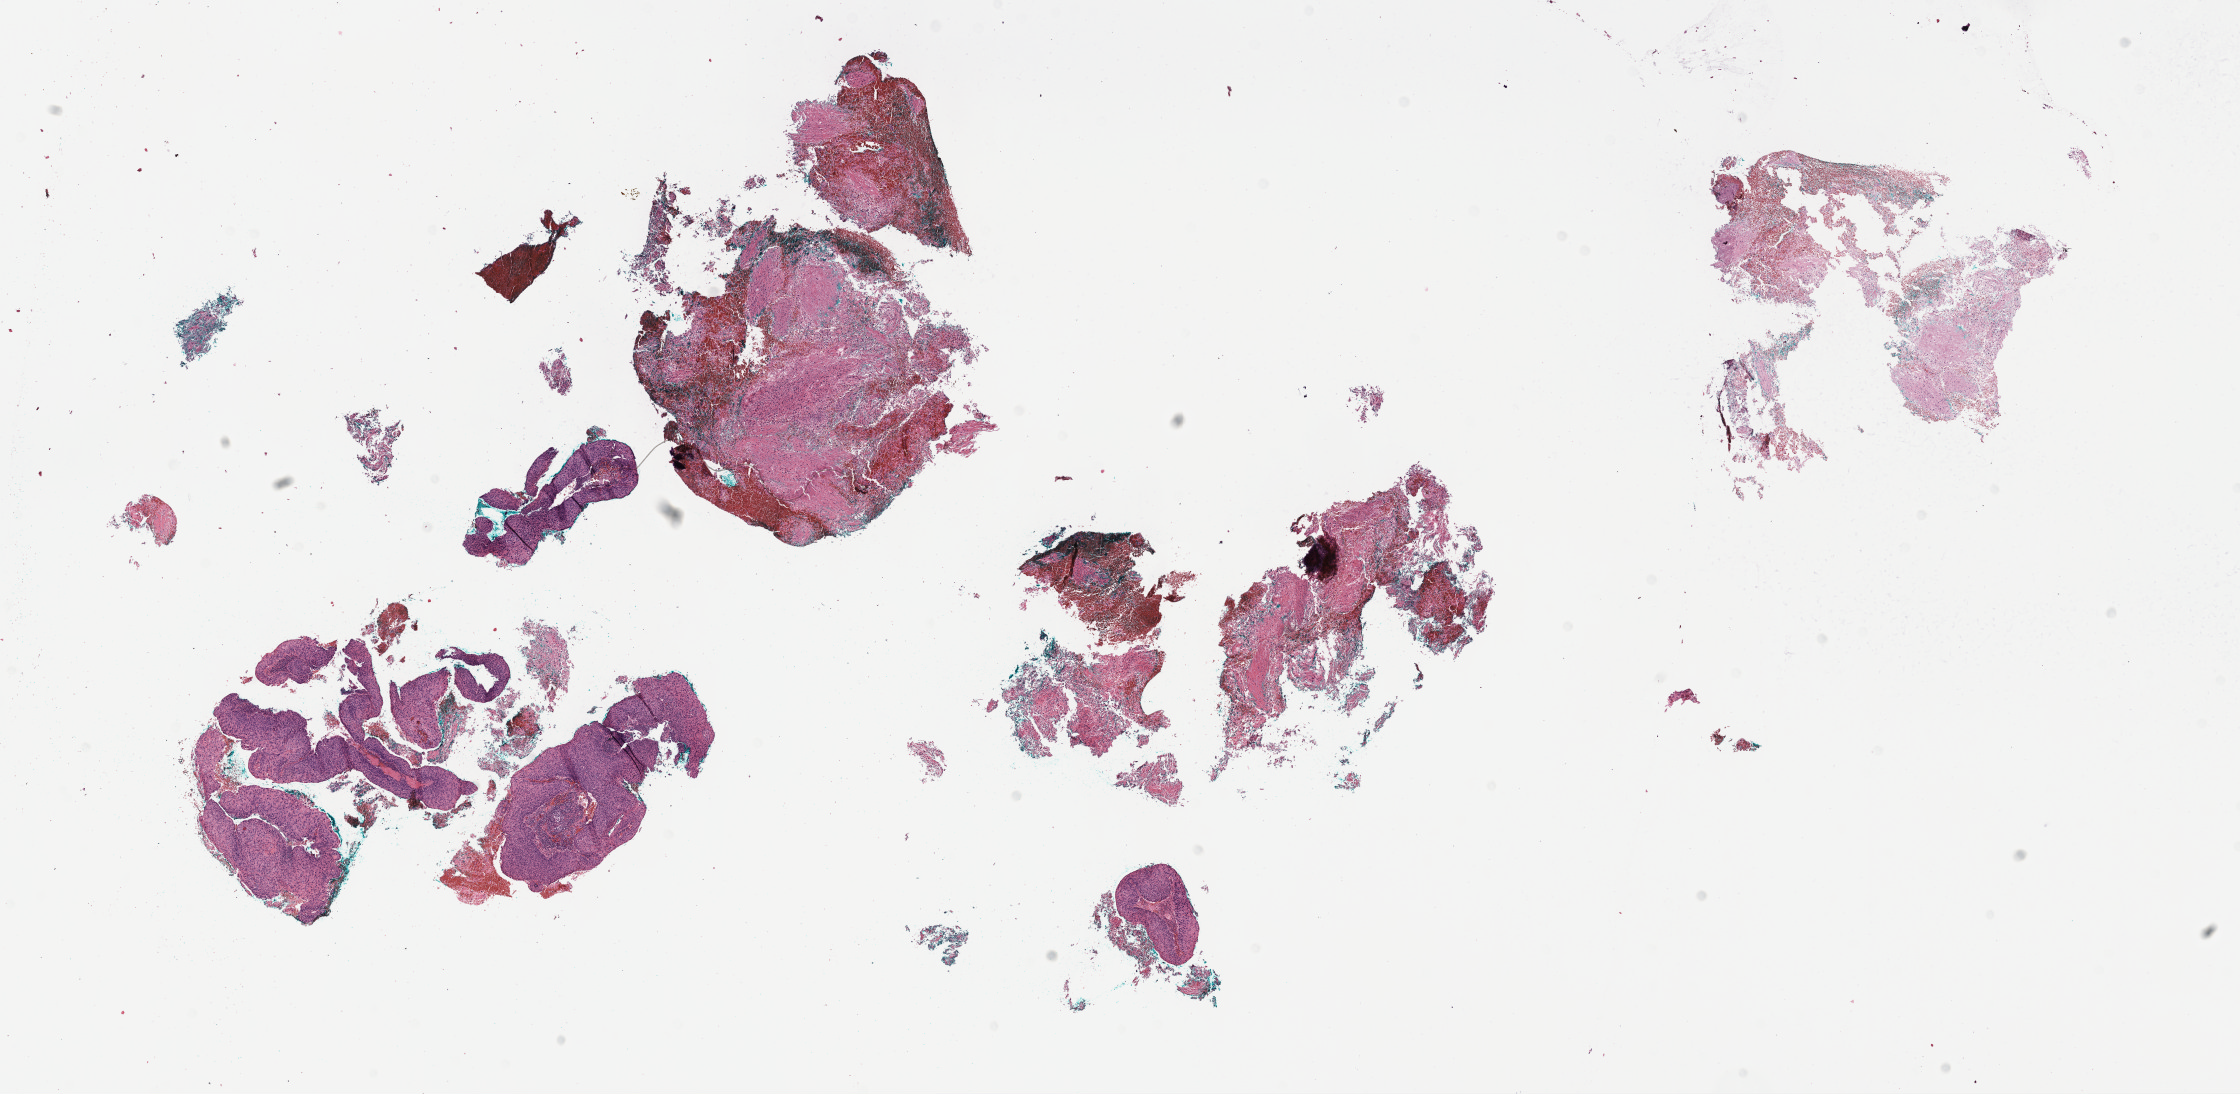
H&E whole-slide image — a low-resolution overview of the entire scanned area, about 18.1 x 8.9 mm. FFPE section. Cervix, primary tumour sample. Female, age 76 years at initial diagnosis. Histologic grade: GX (grade cannot be assessed).
FIGO stage: IIB. Histologic diagnosis: Squamous cell carcinoma, NOS (cervix uteri).